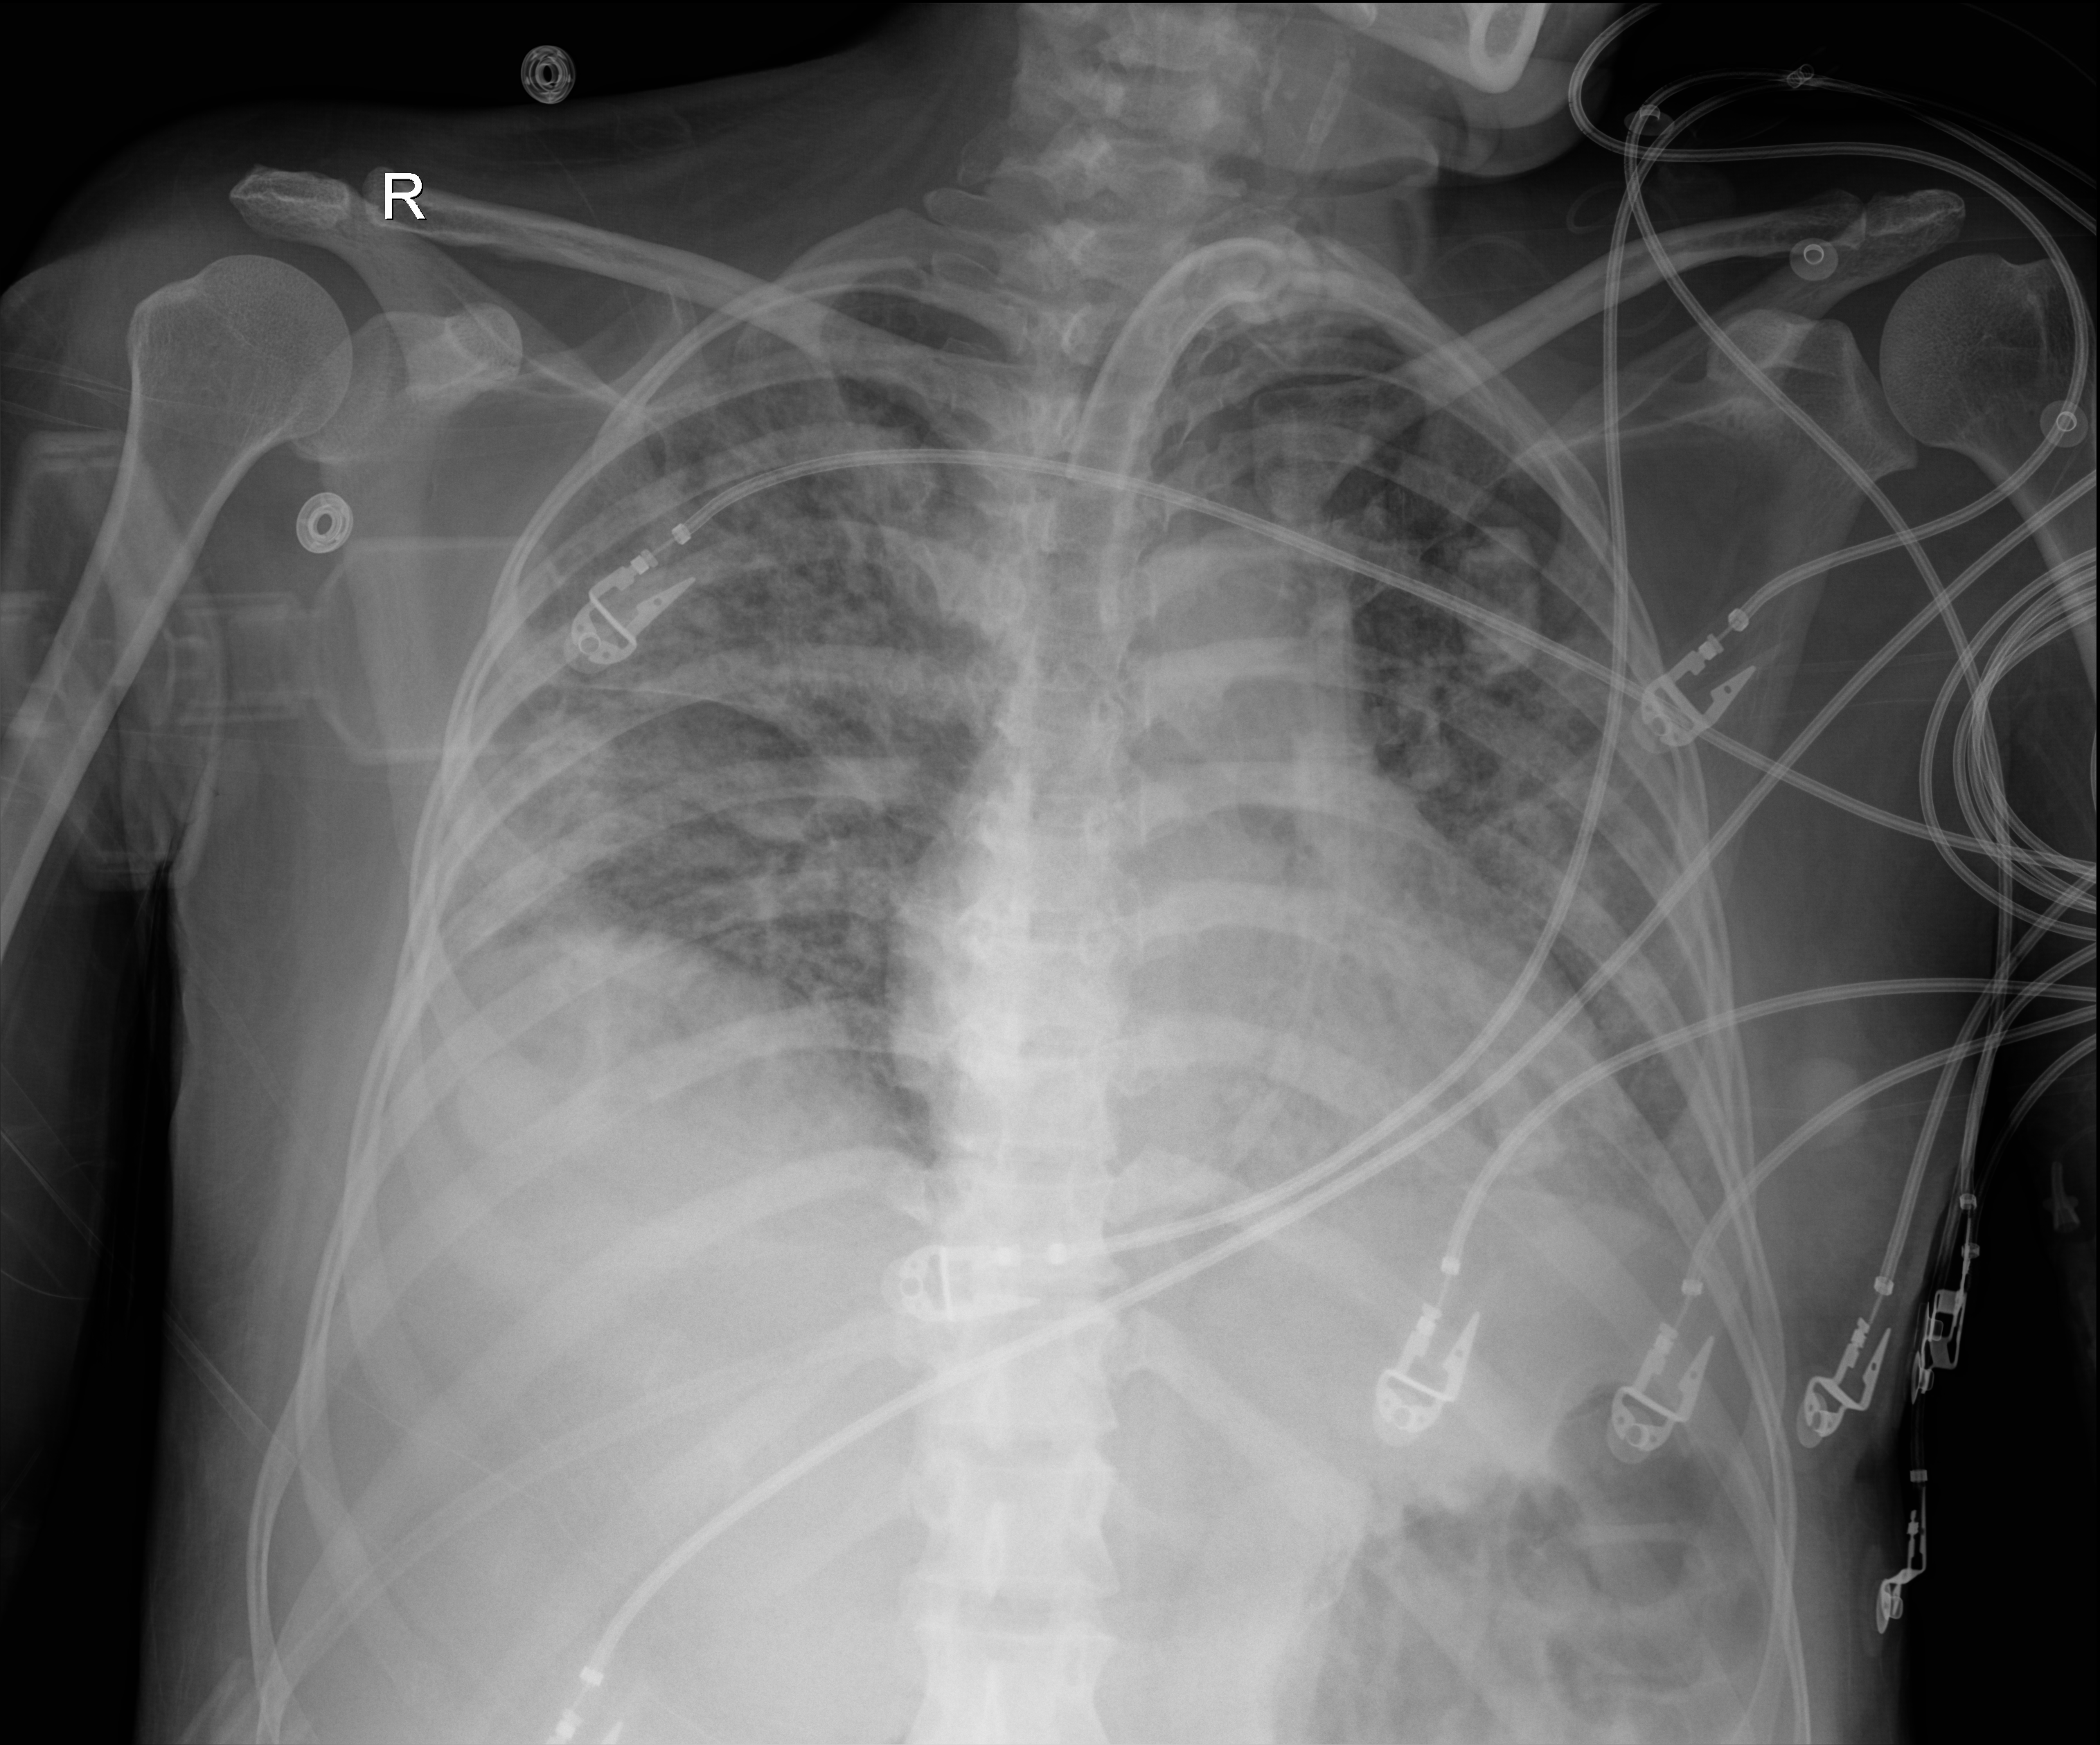
Portable chest radiograph, anteroposterior (AP) projection. Patient hospitalised with COVID-19; female, aged 18–59 years.
Hospital-stay facts (about this admission, not read from this image; timing relative to this image not recorded): admitted to intensive care during this hospital stay: yes; chronic kidney disease (admission record): no; hypertension (admission record): no.